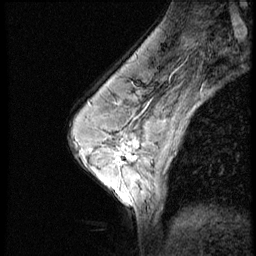
Breast MRI (dynamic contrast-enhanced), one sagittal slice; position 35 of 52 along the scan axis; 3 images stored at this slice position (order not interpretable as contrast timing); 1.5 T; TE 4.2 ms, TR 9 ms; 256 × 256 image matrix, field of view 180 × 180 mm. Female patient, age 50 years. From the clinical record (not read from this slice): setting: breast cancer imaged before/during neoadjuvant chemotherapy; receptor status: HR-positive, HER2-negative.
Structures marked on this image (semi-automatically segmented with operator editing):
- analysis volume of interest (the breast-tissue region the enhancement analysis was run in; not a lesion): bounding box [x1, y1, x2, y2] px = [103, 130, 151, 181]
- tumour enhancement mask (voxels above the 140 % enhancement threshold inside the analysis volume of interest): [124, 139, 139, 149]